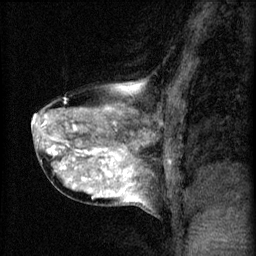
Breast MRI (dynamic contrast-enhanced), one sagittal slice. Position 31 of 60 along the scan axis. 3 images stored at this slice position (order not interpretable as contrast timing). 1.5 T. TE 4.2 ms, TR 8.2 ms. 2 mm slice thickness. 256 × 256 image matrix. Patient: female, 40 years.
Annotated regions visible in this slice (semi-automatic segmentation, software-assisted and operator-edited):
- analysis volume of interest (the breast-tissue region the enhancement analysis was run in; not a lesion): box from (x=31, y=80) to (x=167, y=211) px
- tumour enhancement mask (voxels above the 70 % enhancement threshold inside the analysis volume of interest): (x=32, y=88)–(x=141, y=199)